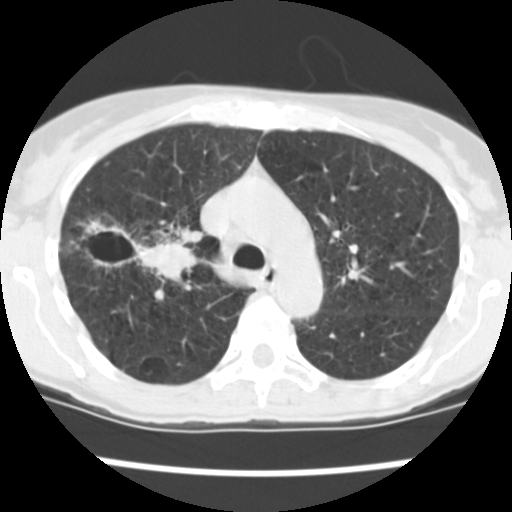
Chest CT (low-dose screening protocol), one axial image, baseline annual screen, lung window (W 1500 / L -600 HU), 2.5 mm slice thickness, 120 kVp, 512 × 512 image matrix. Female, age 60 years at enrolment. Current smoker at enrolment.
Expert reader's lesion annotation, bounding box <83,216,196,284> (left, top, right, bottom; pixels). The screening reader recorded 3 non-calcified nodules or masses ≥4 mm on this exam (right upper lobe, right upper lobe, right lower lobe); which of them this box marks is not recorded. Participant outcome: lung cancer diagnosed 19 days after this screen — non-small cell carcinoma, right upper lobe, stage IV (AJCC 6th edition), 26 mm at pathology.